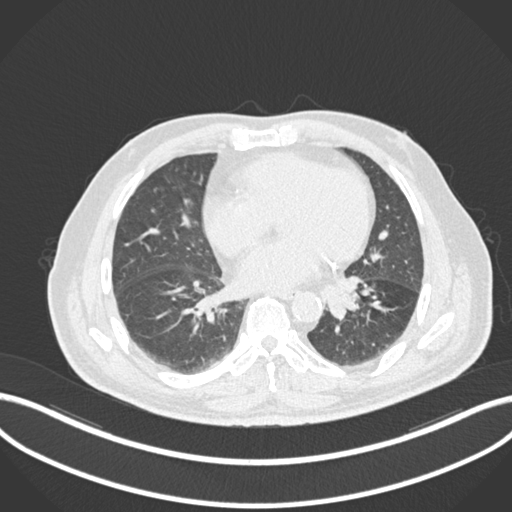
Chest CT, one axial slice; position 47 of 161 along the scan axis; reconstruction kernel B30f; 120 kVp; lung window (W 1500 / L -600 HU); 1 mm slice thickness; 512 × 512 image matrix, field of view 400 × 400 mm. Male patient, age 71 years. Case-level facts recorded for this patient, not image findings: clinical TNM (as recorded): T1b N0 M0.
Annotated regions visible in this slice (rectangle marked by the reading radiologist):
- lung tumour (recorded histology: squamous cell carcinoma): box from (x=325, y=273) to (x=366, y=322) px